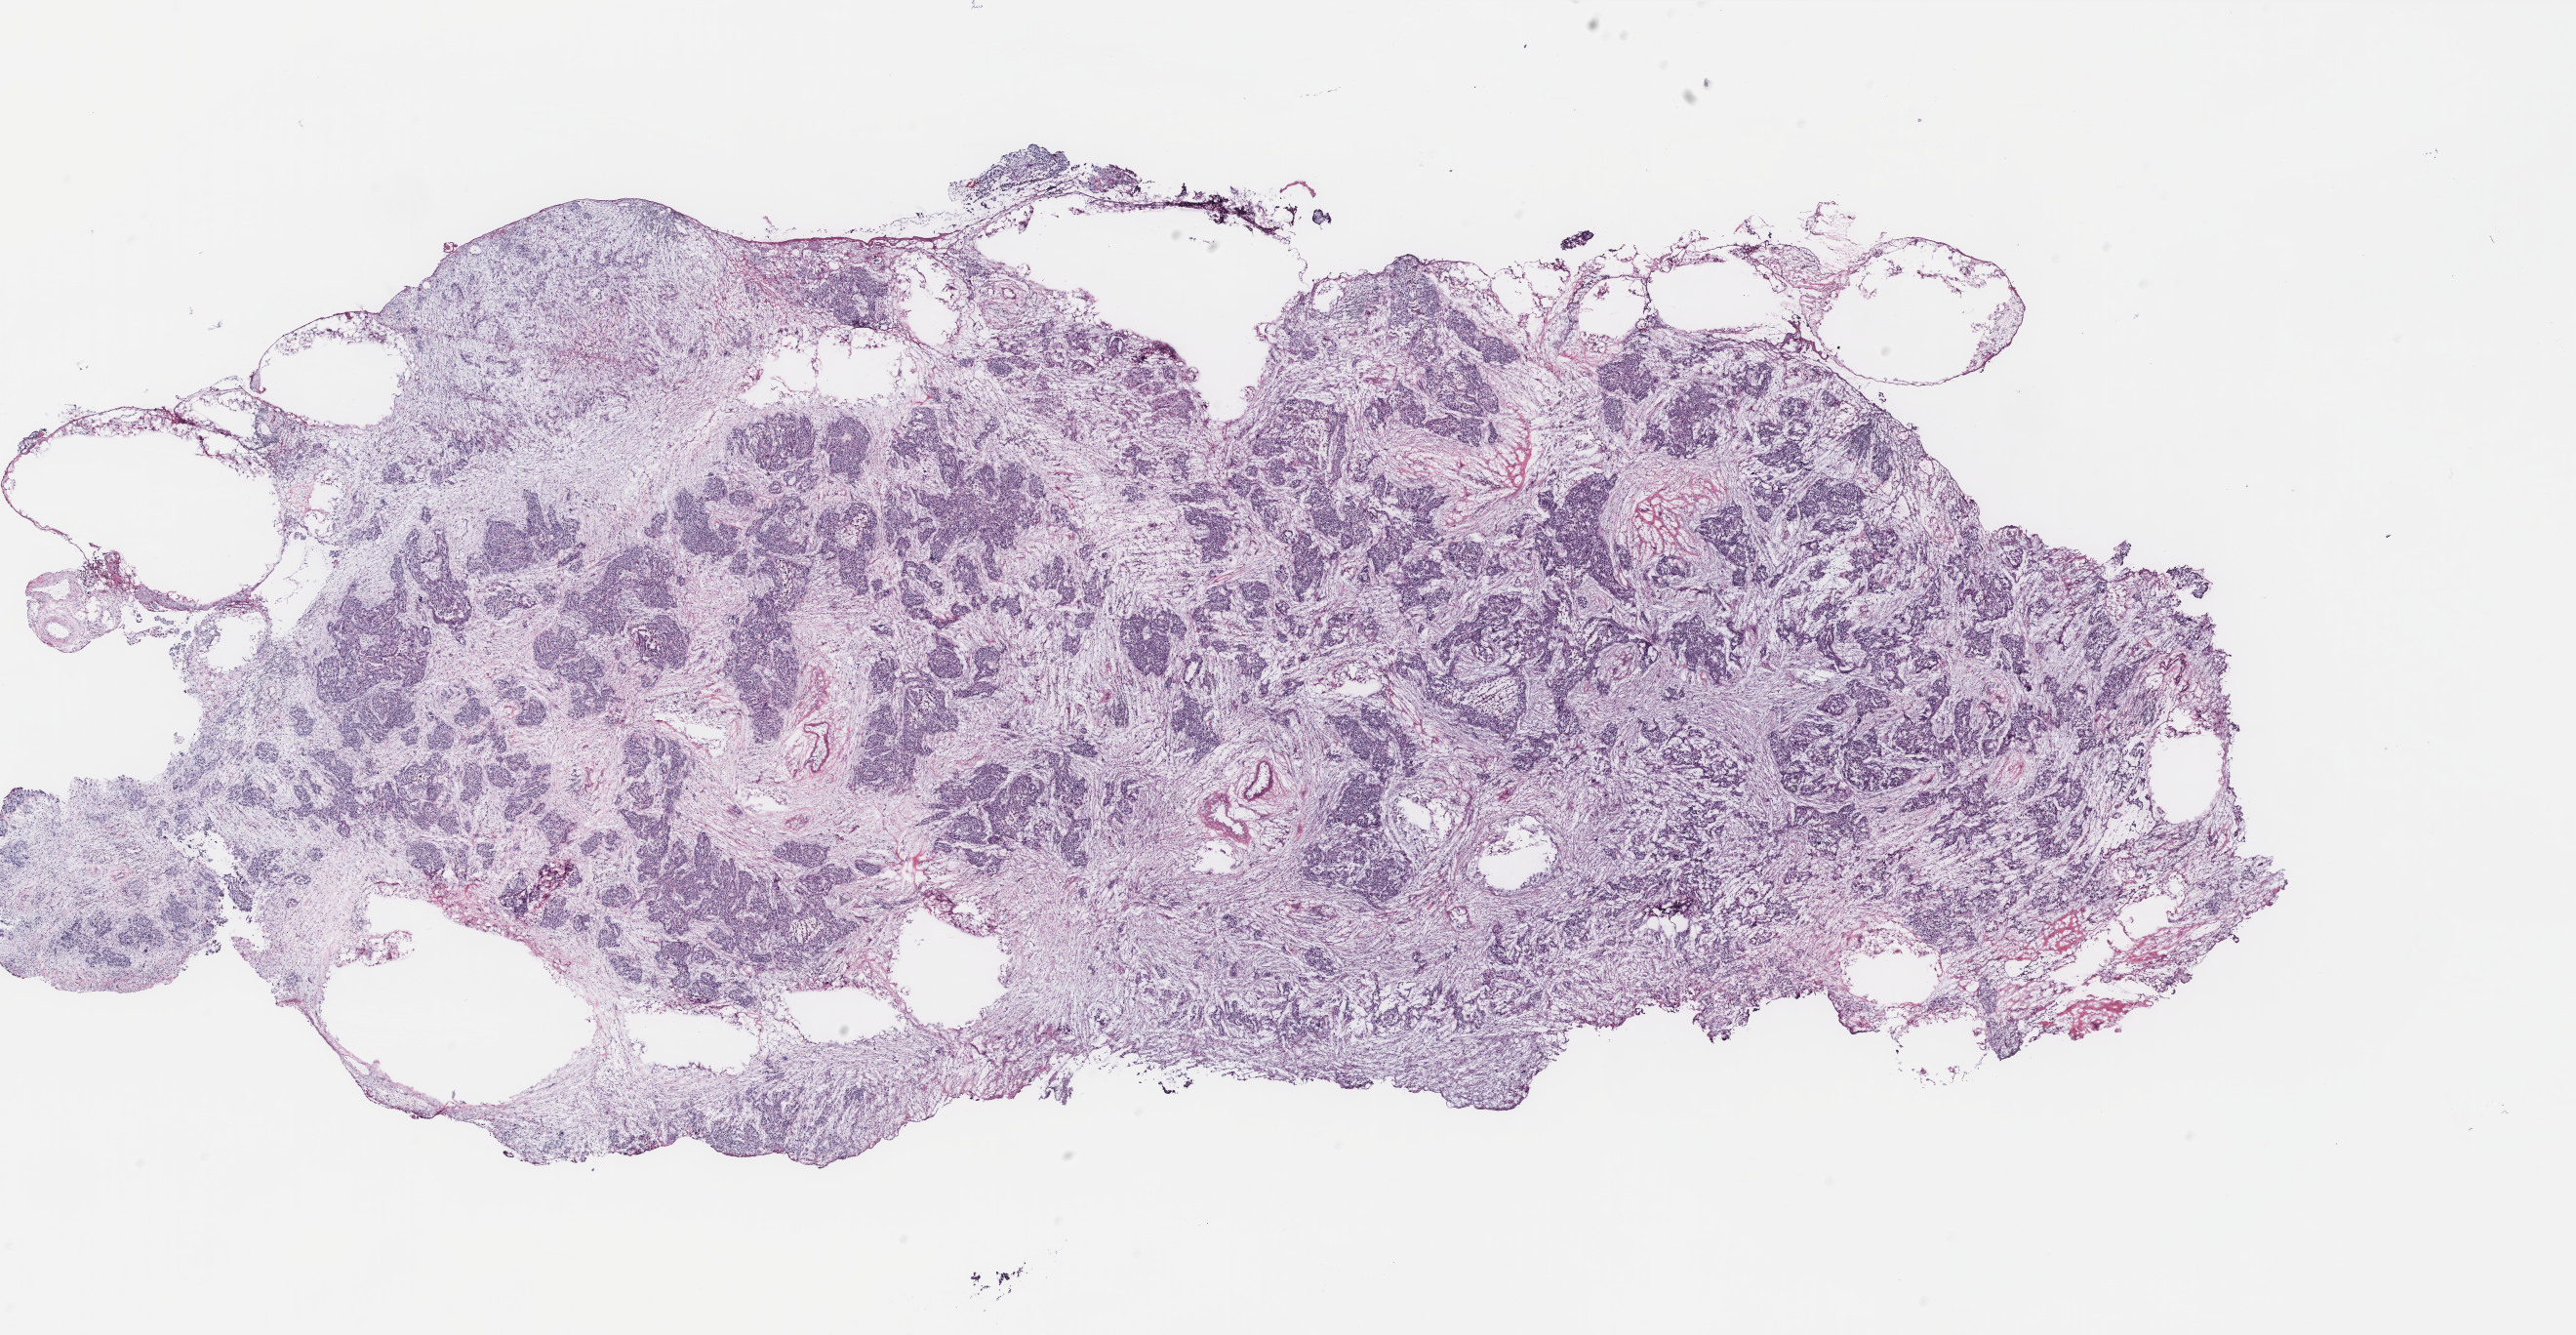
Digitized Hematoxylin and eosin (H&E) stained tissue section (whole slide), shown as a low-resolution overview of the whole scanned area (about 21.1 x 10.9 mm). Ovary, tissue type not recorded. Female patient.
- patient diagnosis: Serous adenocarcinoma, NOS